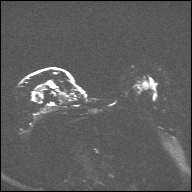
Breast MRI, one axial slice; slice 24 of 32 in the series (ordered by position); diffusion-weighted series; image 2 of 4 stored at this slice position (different b-values; order by instance number); 1.5 T; 4 mm slice thickness; 192 × 192 image matrix, field of view 360 × 360 mm. Female patient.
Outlined on this slice (outlined manually by an expert reader):
- tumour on diffusion-weighted imaging: box from (x=36, y=83) to (x=46, y=101) px